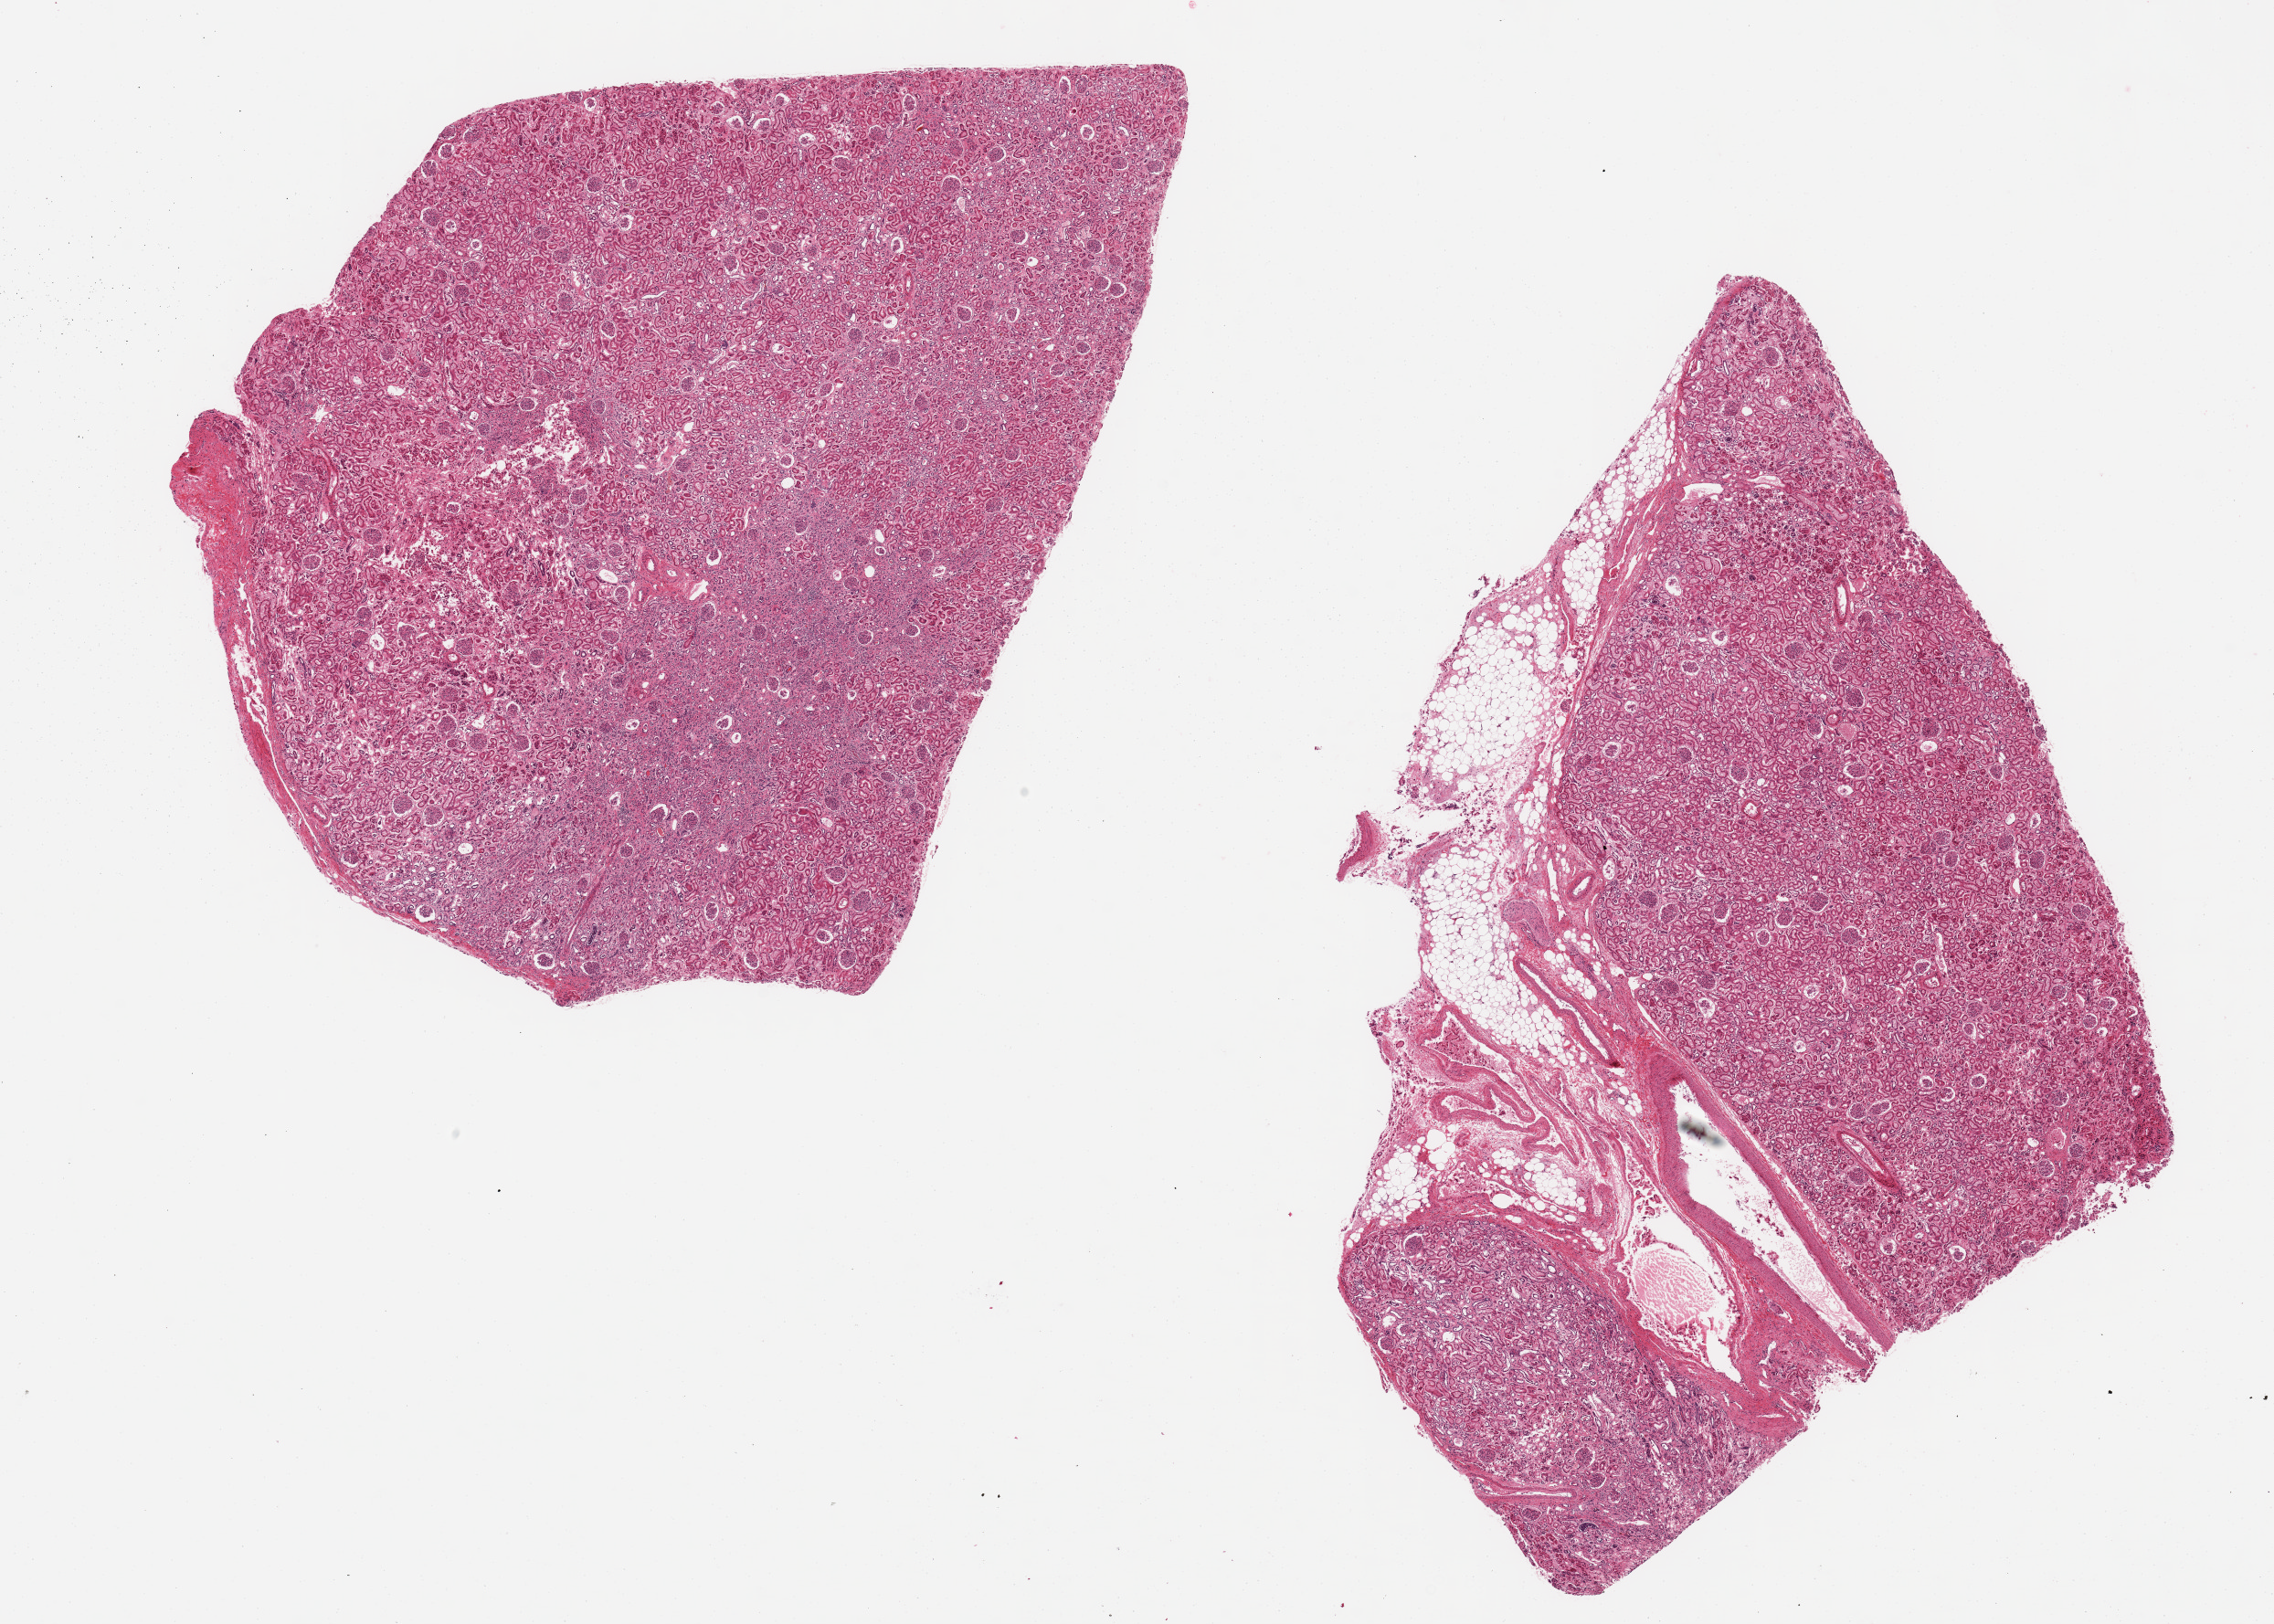
Whole-slide image, H&E stain, brightfield, shown as a low-resolution overview of the whole scanned area (about 19.7 x 14.1 mm), PAXgene-fixed, paraffin-embedded tissue, sampled site (target tissue): renal cortex, tissue donor sample. Donor sex: female.
Reviewer comment on this tissue sample: 2 ~8x7mm aliquots???renal cortex, not medulla.